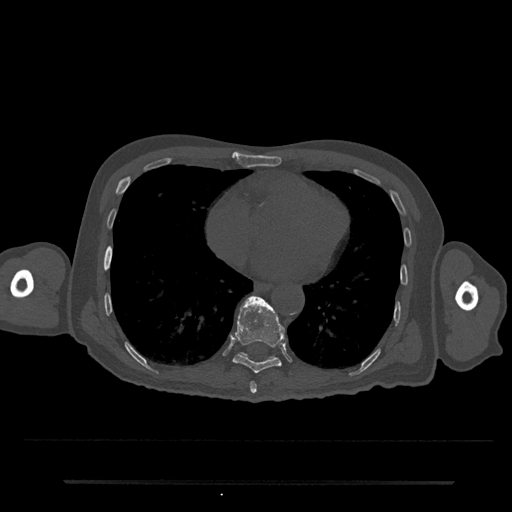
CT including the spine, one axial slice; slice 359 of 797 in the series (ordered by position); reconstruction kernel Br40s/3; bone window (W 1800 / L 400 HU); 0.5 mm slice thickness; 512 × 512 image matrix, field of view 427 × 427 mm. Patient: male, 74 years. Case-level facts recorded for this patient, not image findings: primary cancer: prostate.
Outlined on this slice (semi-automatically segmented with operator editing):
- T10 vertebra: box from (x=241, y=353) to (x=247, y=356) px
- T8 vertebra: (x=250, y=382)–(x=257, y=394)
- T9 vertebra: (x=233, y=296)–(x=285, y=374)